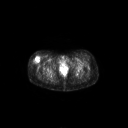
FDG PET of an extremity soft-tissue mass (from a PET/CT study), one axial slice. Slice 55 of 267 in the series (ordered by position). 3.27 mm slice thickness. 128 × 128 image matrix, field of view 700 × 700 mm. Female patient, age 34 years. Case-level facts recorded for this patient, not image findings: histological type: synovial sarcoma; grade: intermediate; site of the primary tumour: right thigh.
Annotated regions visible in this slice (expert contour drawn on MRI and transferred to this co-registered scan by the dataset authors):
- gross tumour volume including surrounding oedema: box from (x=33, y=56) to (x=40, y=63) px
- gross tumour volume (mass): (x=32, y=56)–(x=40, y=63)